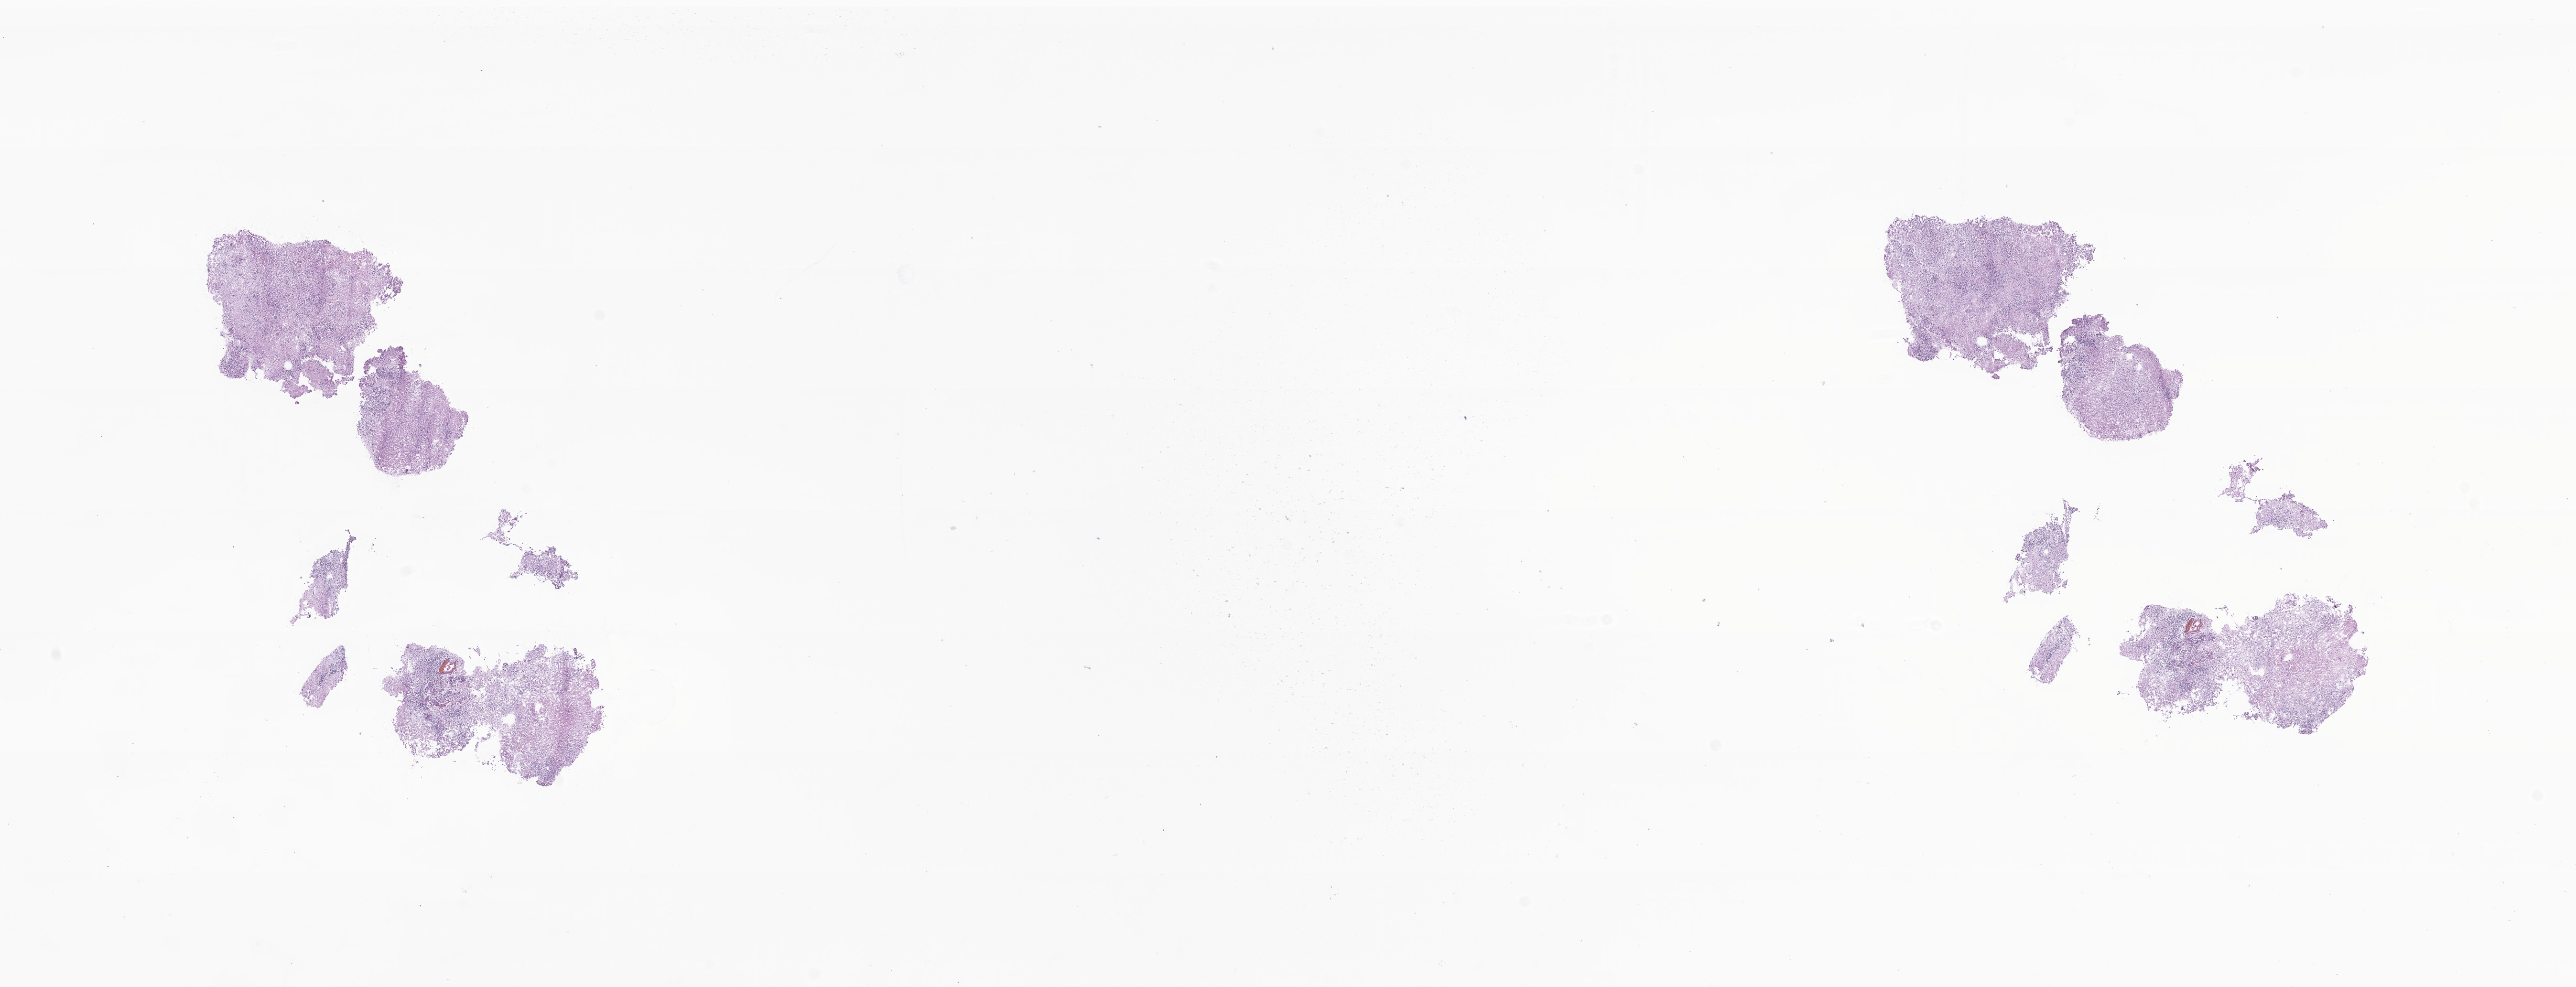
Digitized hematoxylin and eosin (H&E)-stained section of tumor tissue from the brain, whole scanned area (about 22.7 x 8.7 mm) shown as a low-resolution overview. Frozen section (OCT-embedded). Female patient, age 36 months (3 years).
Recorded diagnosis: Medulloblastoma, NOS.